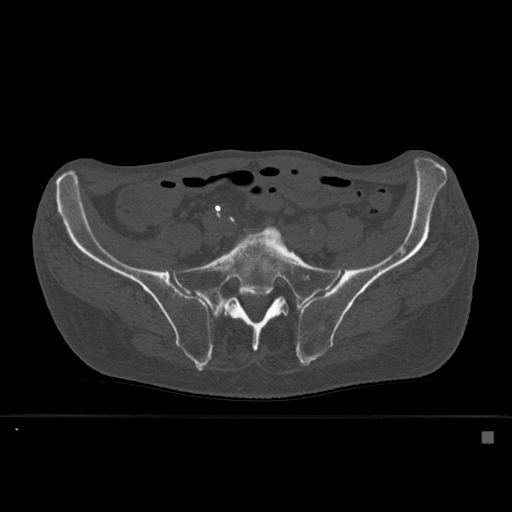
CT including the spine, one axial slice; position 156 of 527 along the scan axis; bone window (W 1800 / L 400 HU); 1.5 mm slice thickness; 512 × 512 image matrix, field of view 373 × 373 mm. Male patient, age 78 years. Case-level facts recorded for this patient, not image findings: primary cancer: prostate.
Outlined on this slice (semi-automatically segmented with operator editing):
- L5 vertebra: bounding box (x1, y1, x2, y2) in pixels: (282, 302, 289, 314)